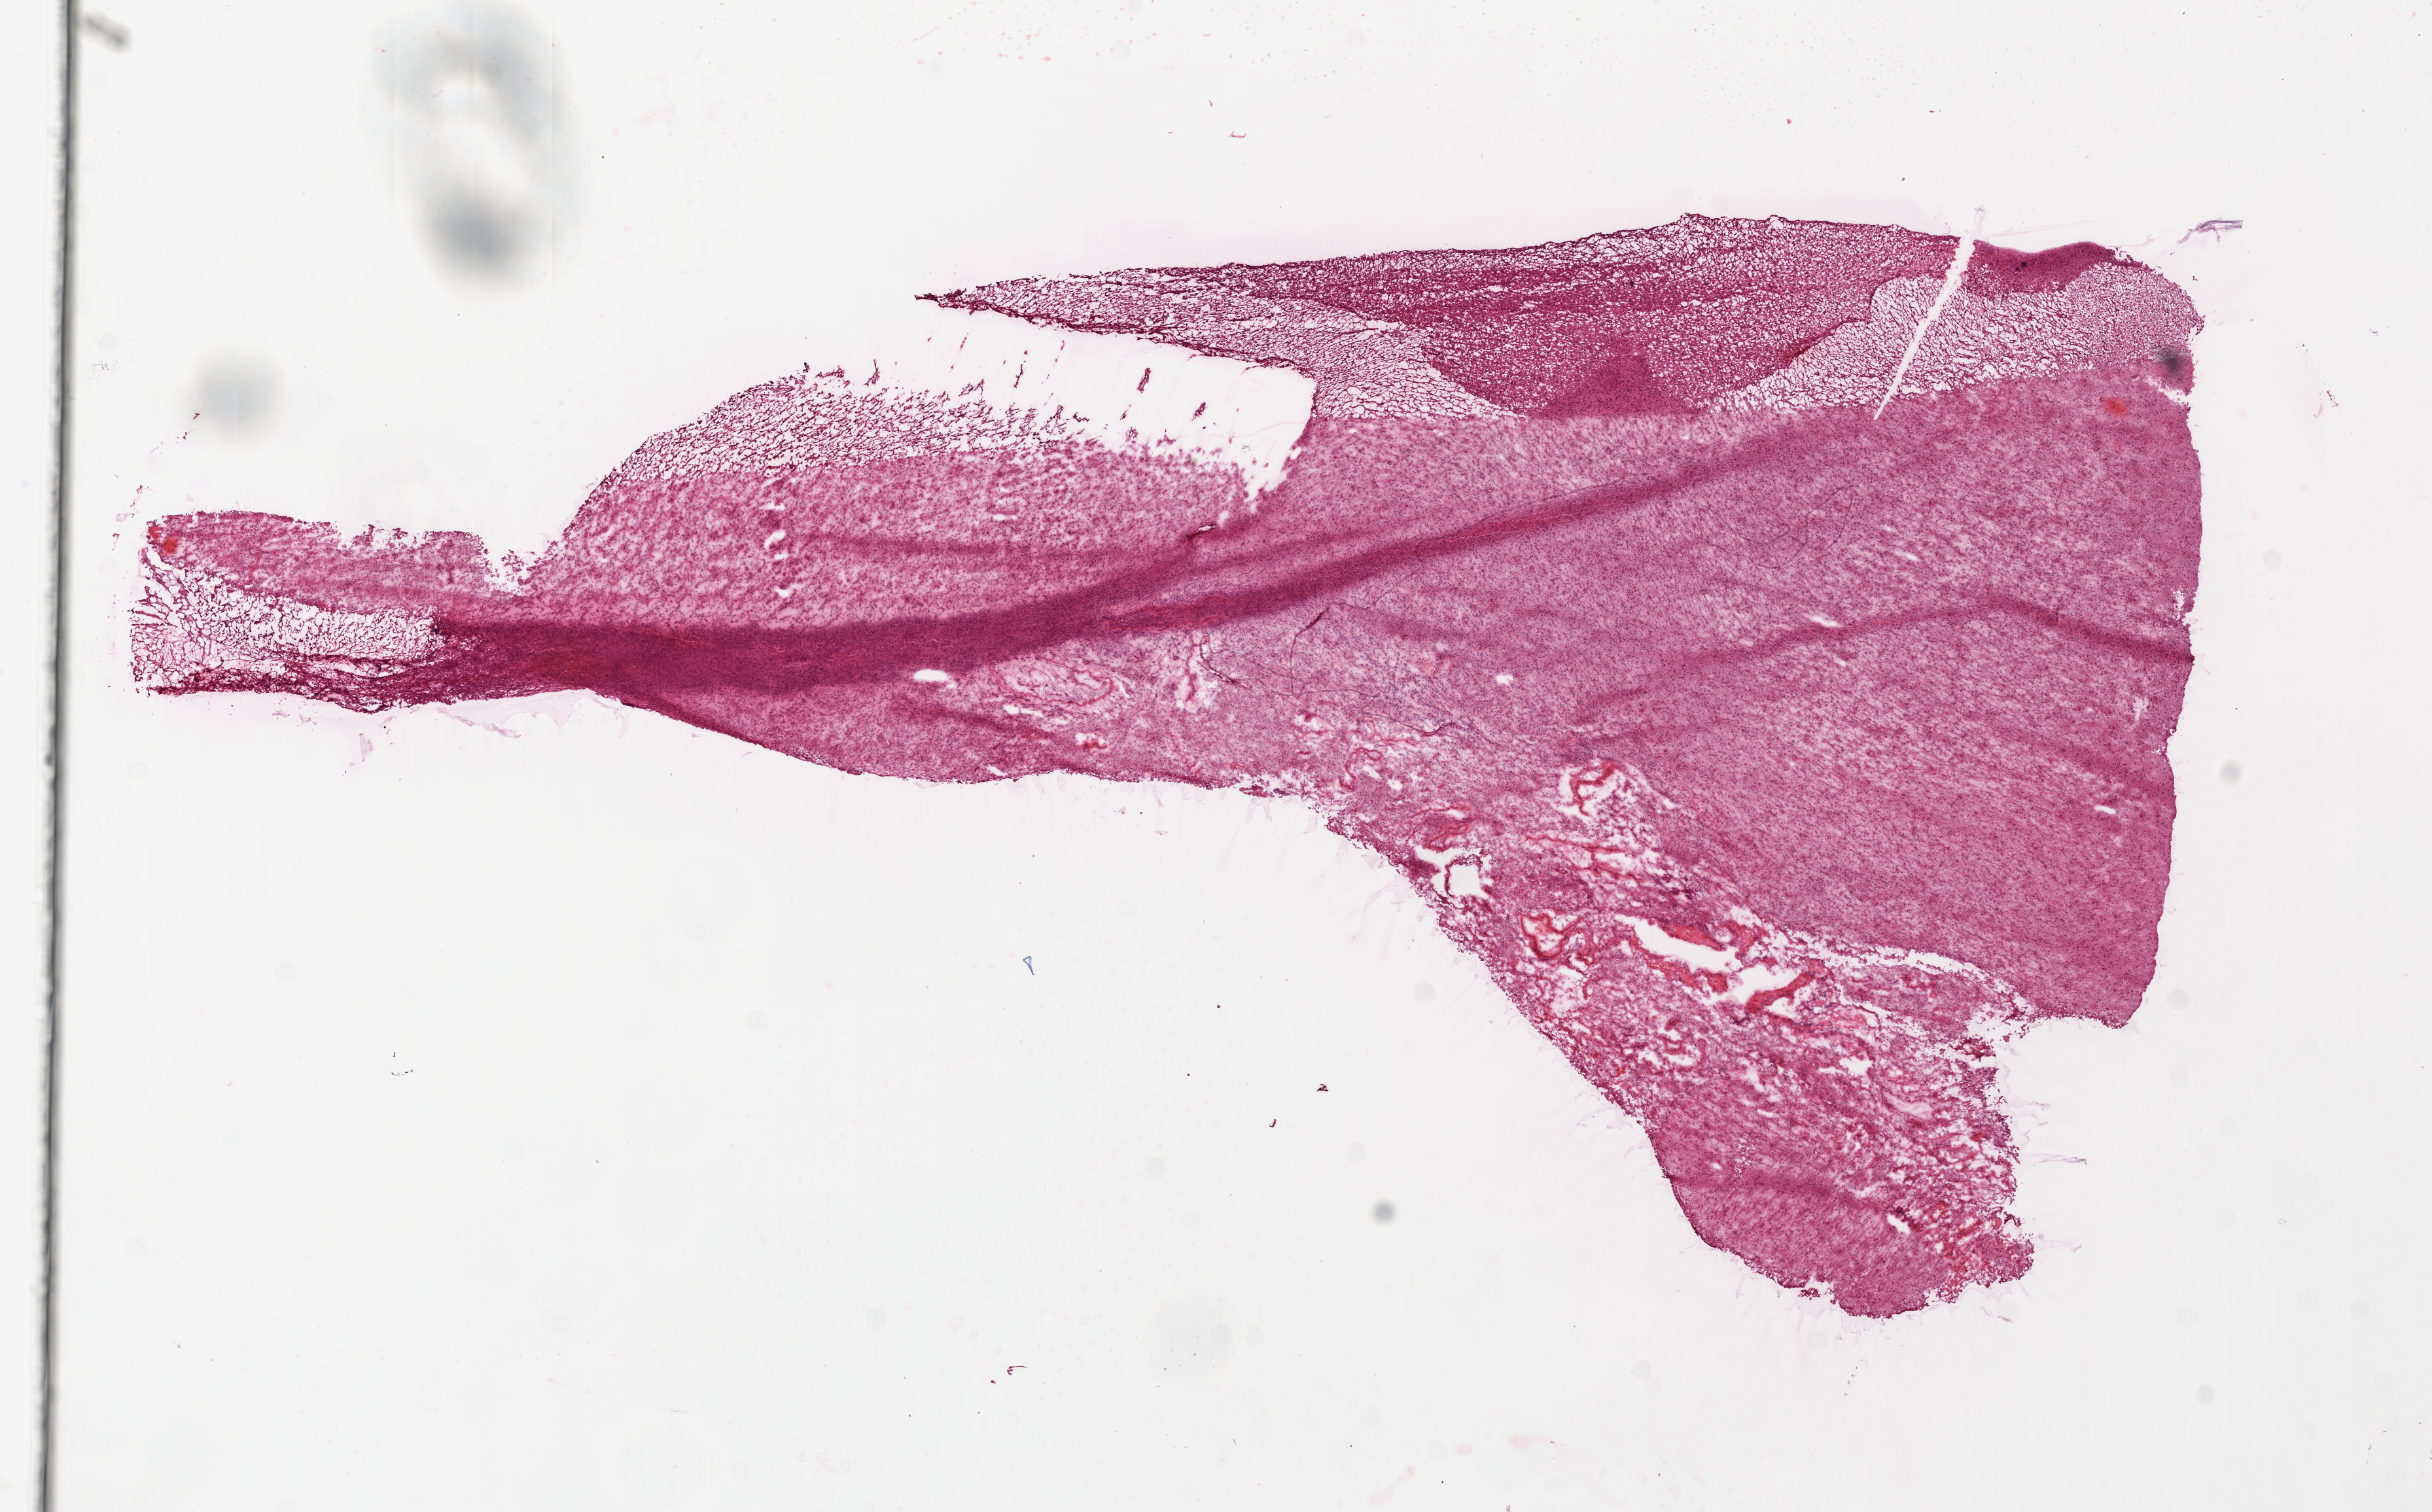
H&E-stained whole-slide image — a low-resolution overview of the entire scanned area, about 15.0 x 9.3 mm (acquisition: 20x scan), frozen section, brain, primary tumour sample. Female, age 65 years at initial diagnosis. Composition of this section per pathologist review: tumour cells 85%, tumour nuclei 90%, normal cells 5%, stromal cells 10%, necrosis 0%.
Histologic diagnosis: Glioblastoma.